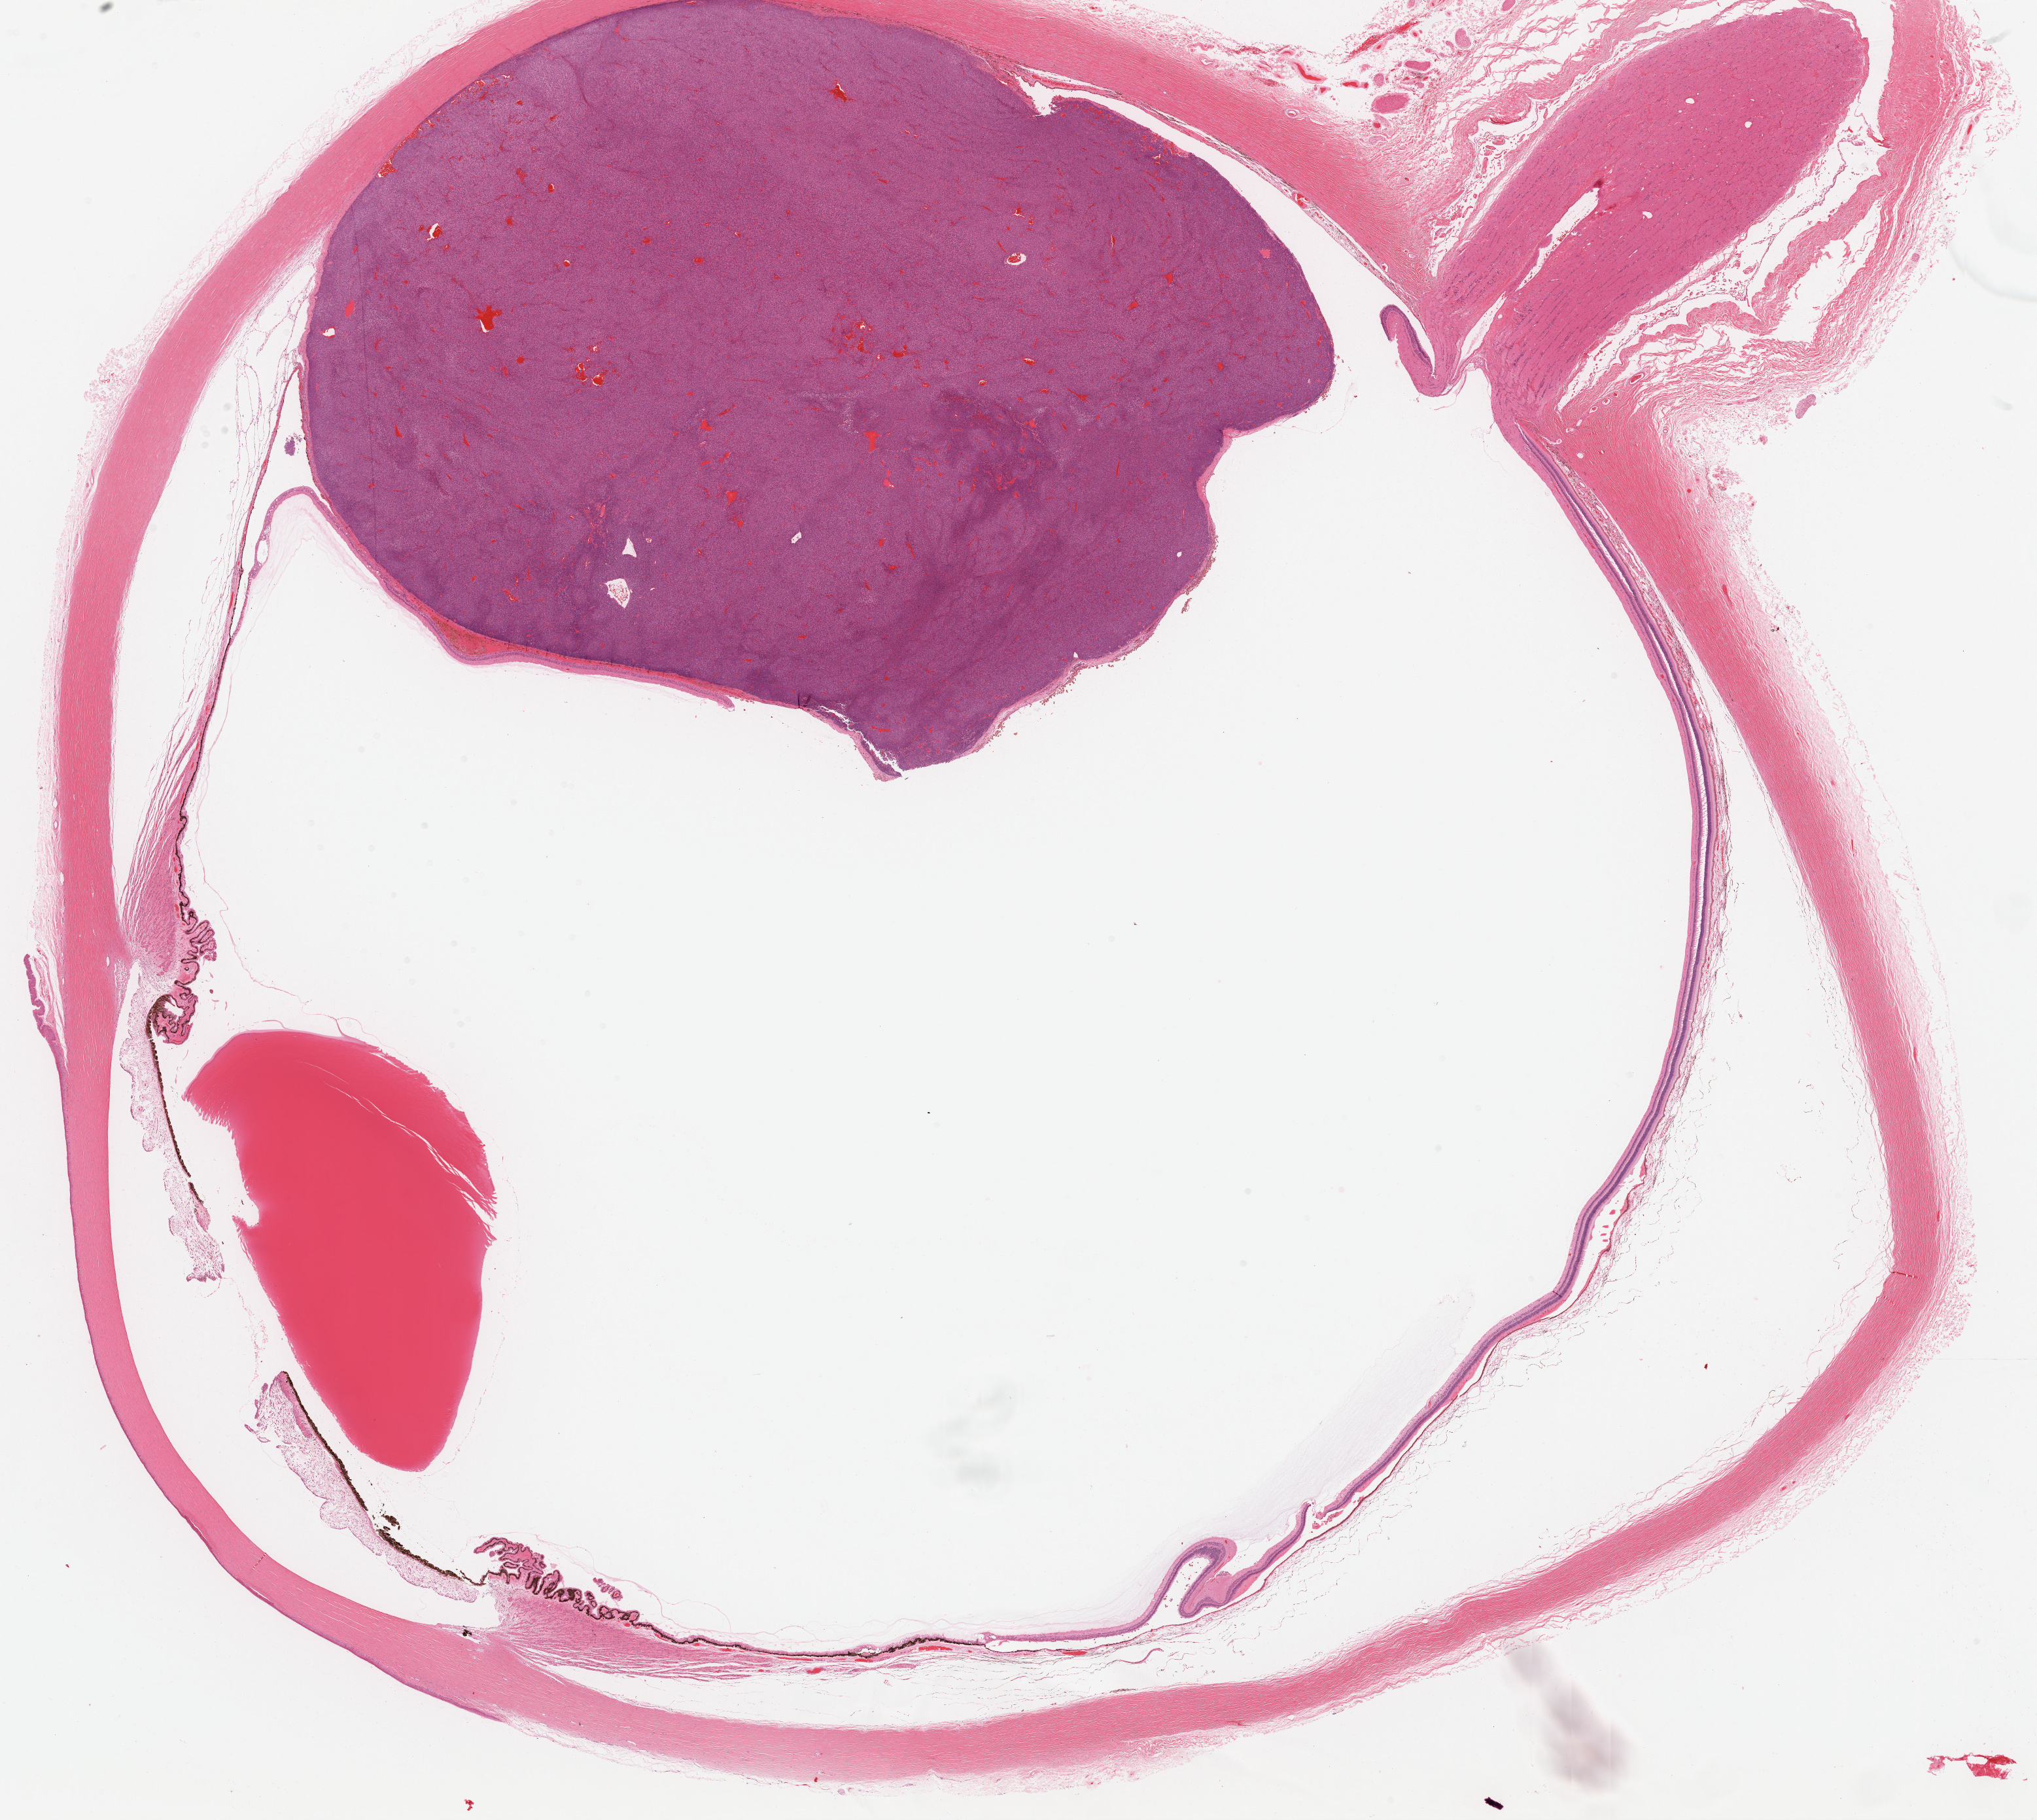
Whole-slide histology image, Hematoxylin and eosin (H&E) stained, low-resolution overview of the scanned area, about 25.1 x 22.4 mm, formalin-fixed paraffin-embedded (FFPE) diagnostic section, uvea, primary tumour sample. Male, age 53 years at initial diagnosis.
Histologic diagnosis: Mixed epithelioid and spindle cell melanoma (choroid). Laterality: left. AJCC pathologic stage: IIB.